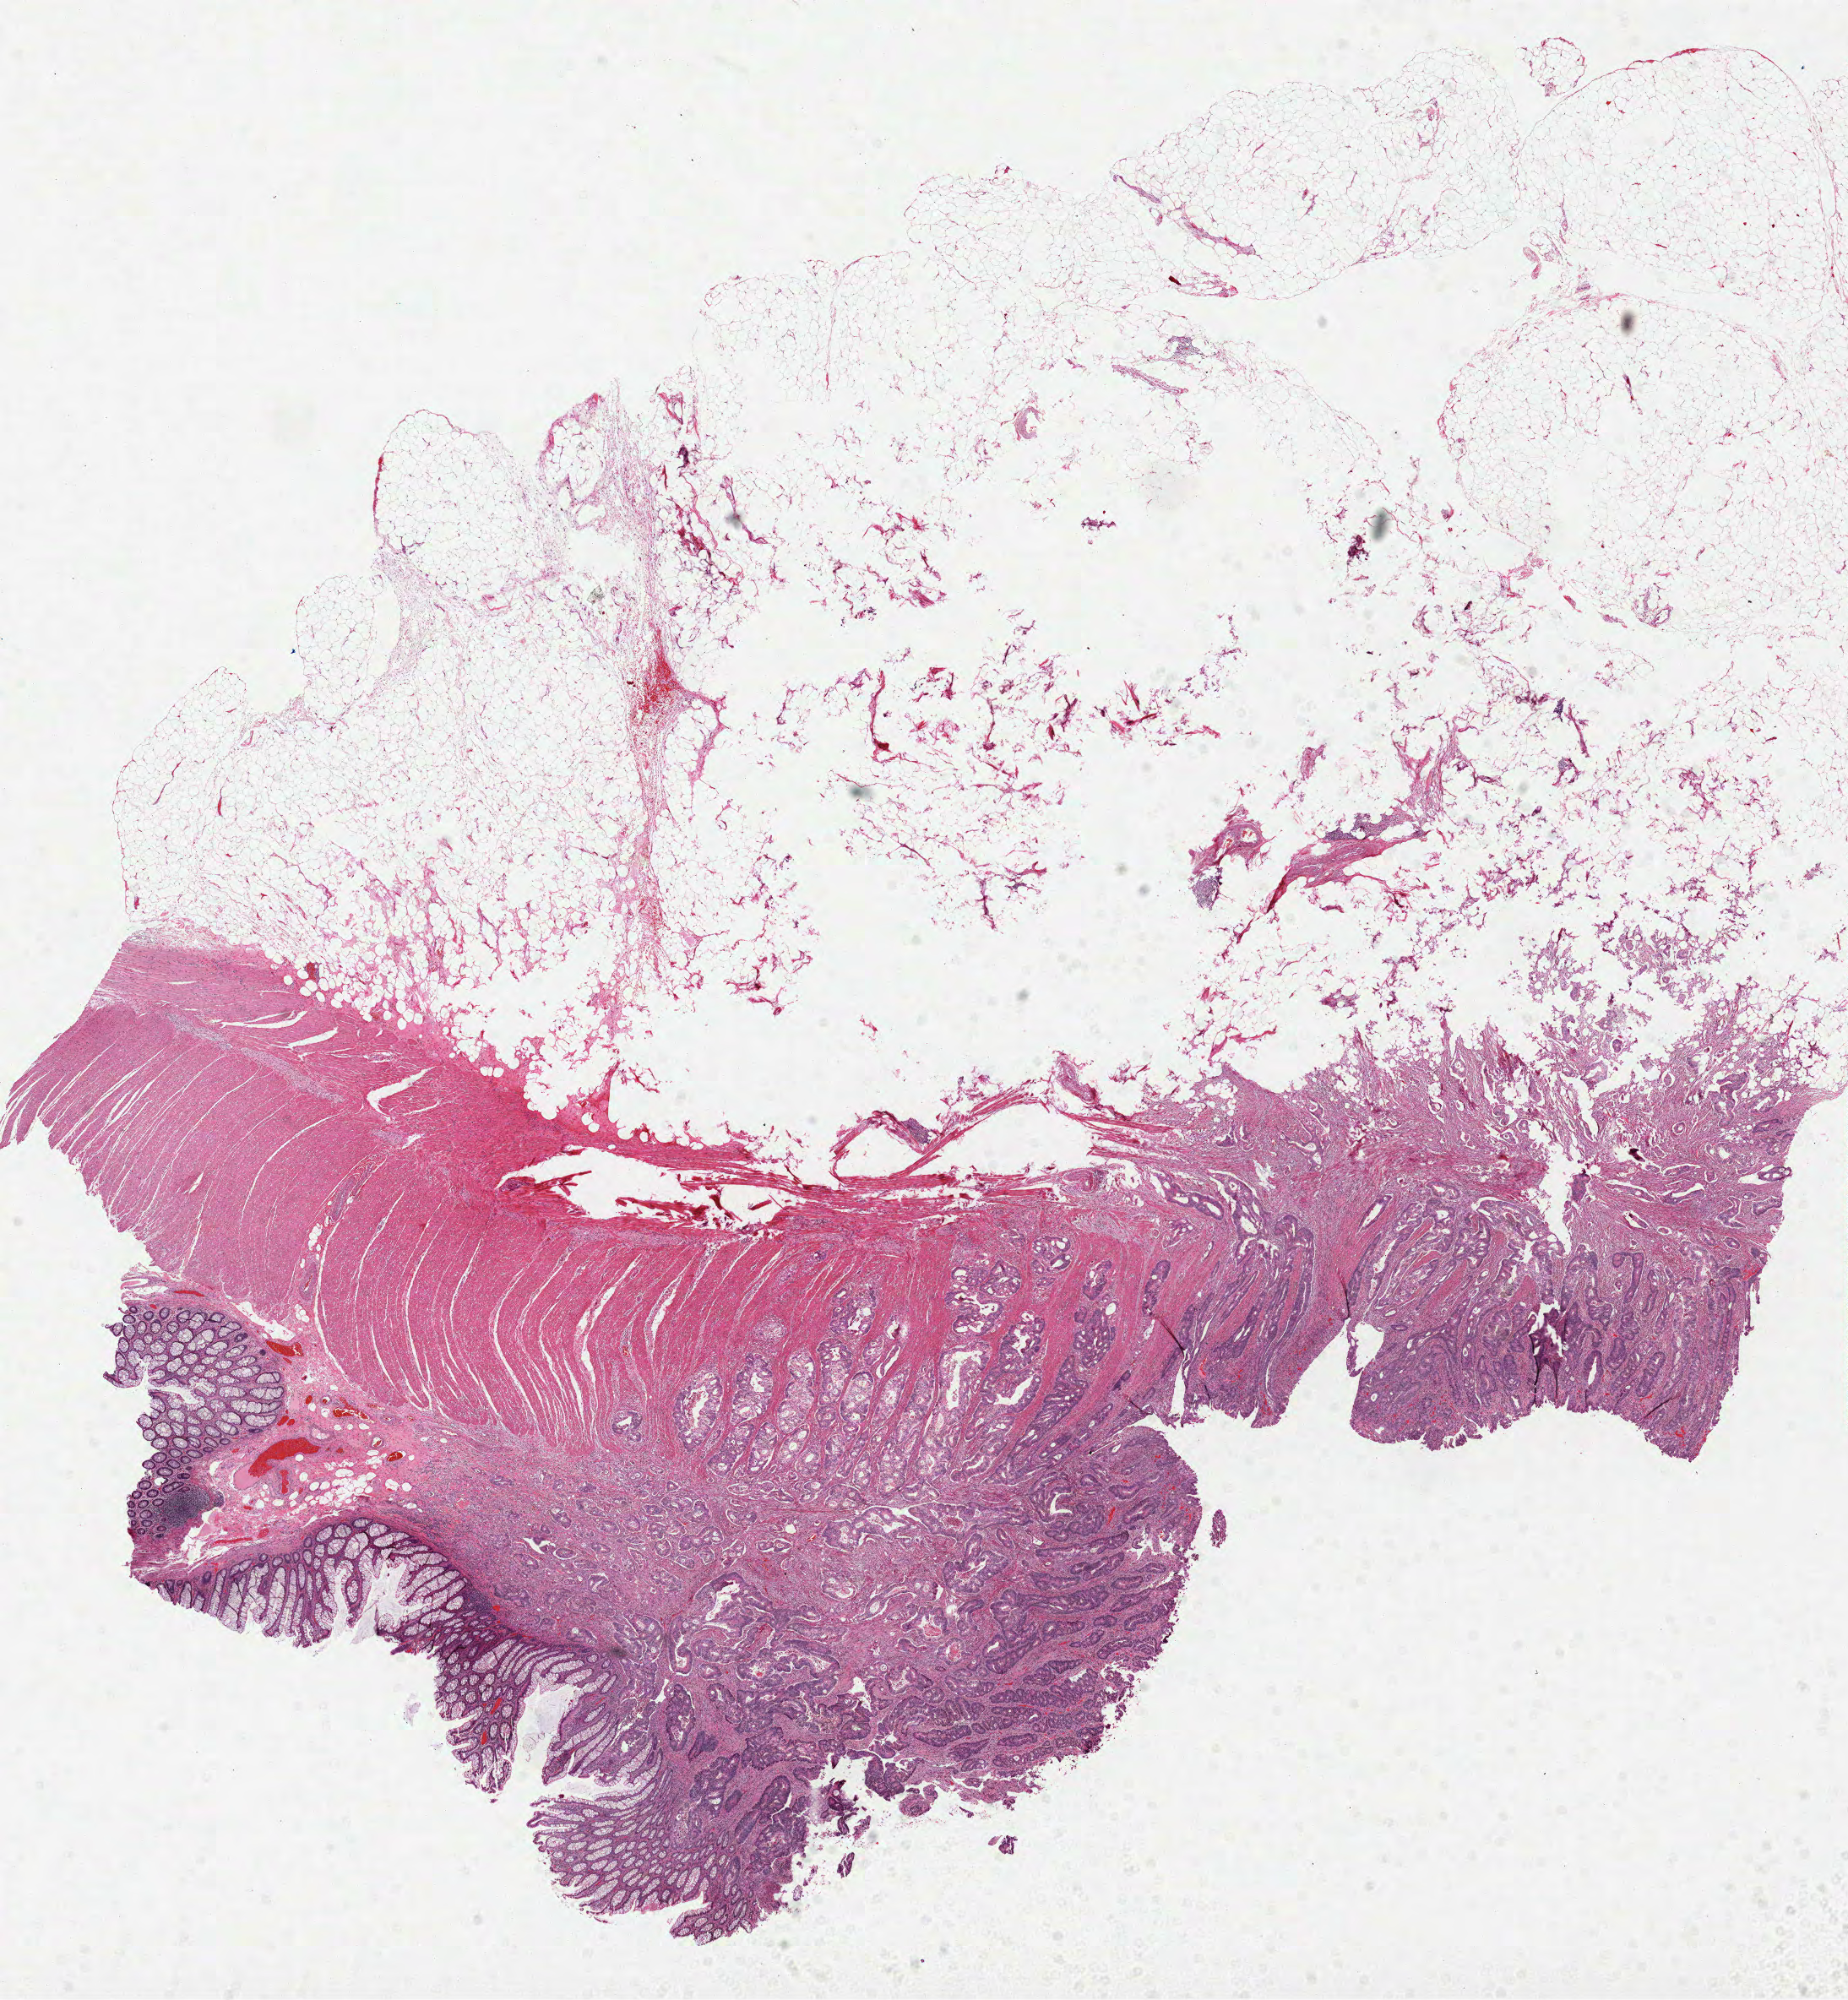
Whole-slide histology image, Hematoxylin and eosin (H&E) stained, low-resolution overview of the scanned area, about 17.6 x 19.1 mm (from a 40x scan), formalin-fixed paraffin-embedded (FFPE) diagnostic section, rectum, primary tumour sample. Patient: male, age at initial diagnosis 68 years.
Pathologic diagnosis: Adenocarcinoma, NOS (rectosigmoid junction).